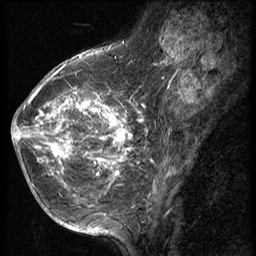
Breast MRI (dynamic contrast-enhanced), one sagittal slice. Slice 23 of 56 in the series (ordered by position). 3 images stored at this slice position (order not interpretable as contrast timing). 1.5 T. TE 4.2 ms, TR 9 ms. 2.5 mm slice thickness. 256 × 256 image matrix, field of view 180 × 180 mm. Female patient, age 49 years. Case-level facts recorded for this patient, not image findings: setting: breast cancer imaged before/during neoadjuvant chemotherapy; receptor status: HER2-positive.
Structures marked on this image (semi-automatic segmentation, software-assisted and operator-edited):
- analysis volume of interest (the breast-tissue region the enhancement analysis was run in; not a lesion): bounding box <13,79,134,203> (left, top, right, bottom; pixels)
- tumour enhancement mask (voxels above the 140 % enhancement threshold inside the analysis volume of interest): <13,82,133,186>